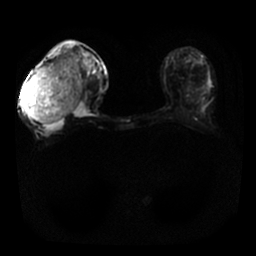
Breast MRI, one axial slice. Slice 5 of 25 in the series (ordered by position). Diffusion-weighted series; image 2 of 4 stored at this slice position (different b-values; order by instance number). 1.5 T. 256 × 256 image matrix, field of view 340 × 340 mm. Female patient.
Annotated regions visible in this slice (manually delineated by an expert):
- tumour on diffusion-weighted imaging: bounding box <27,57,81,125> (left, top, right, bottom; pixels)